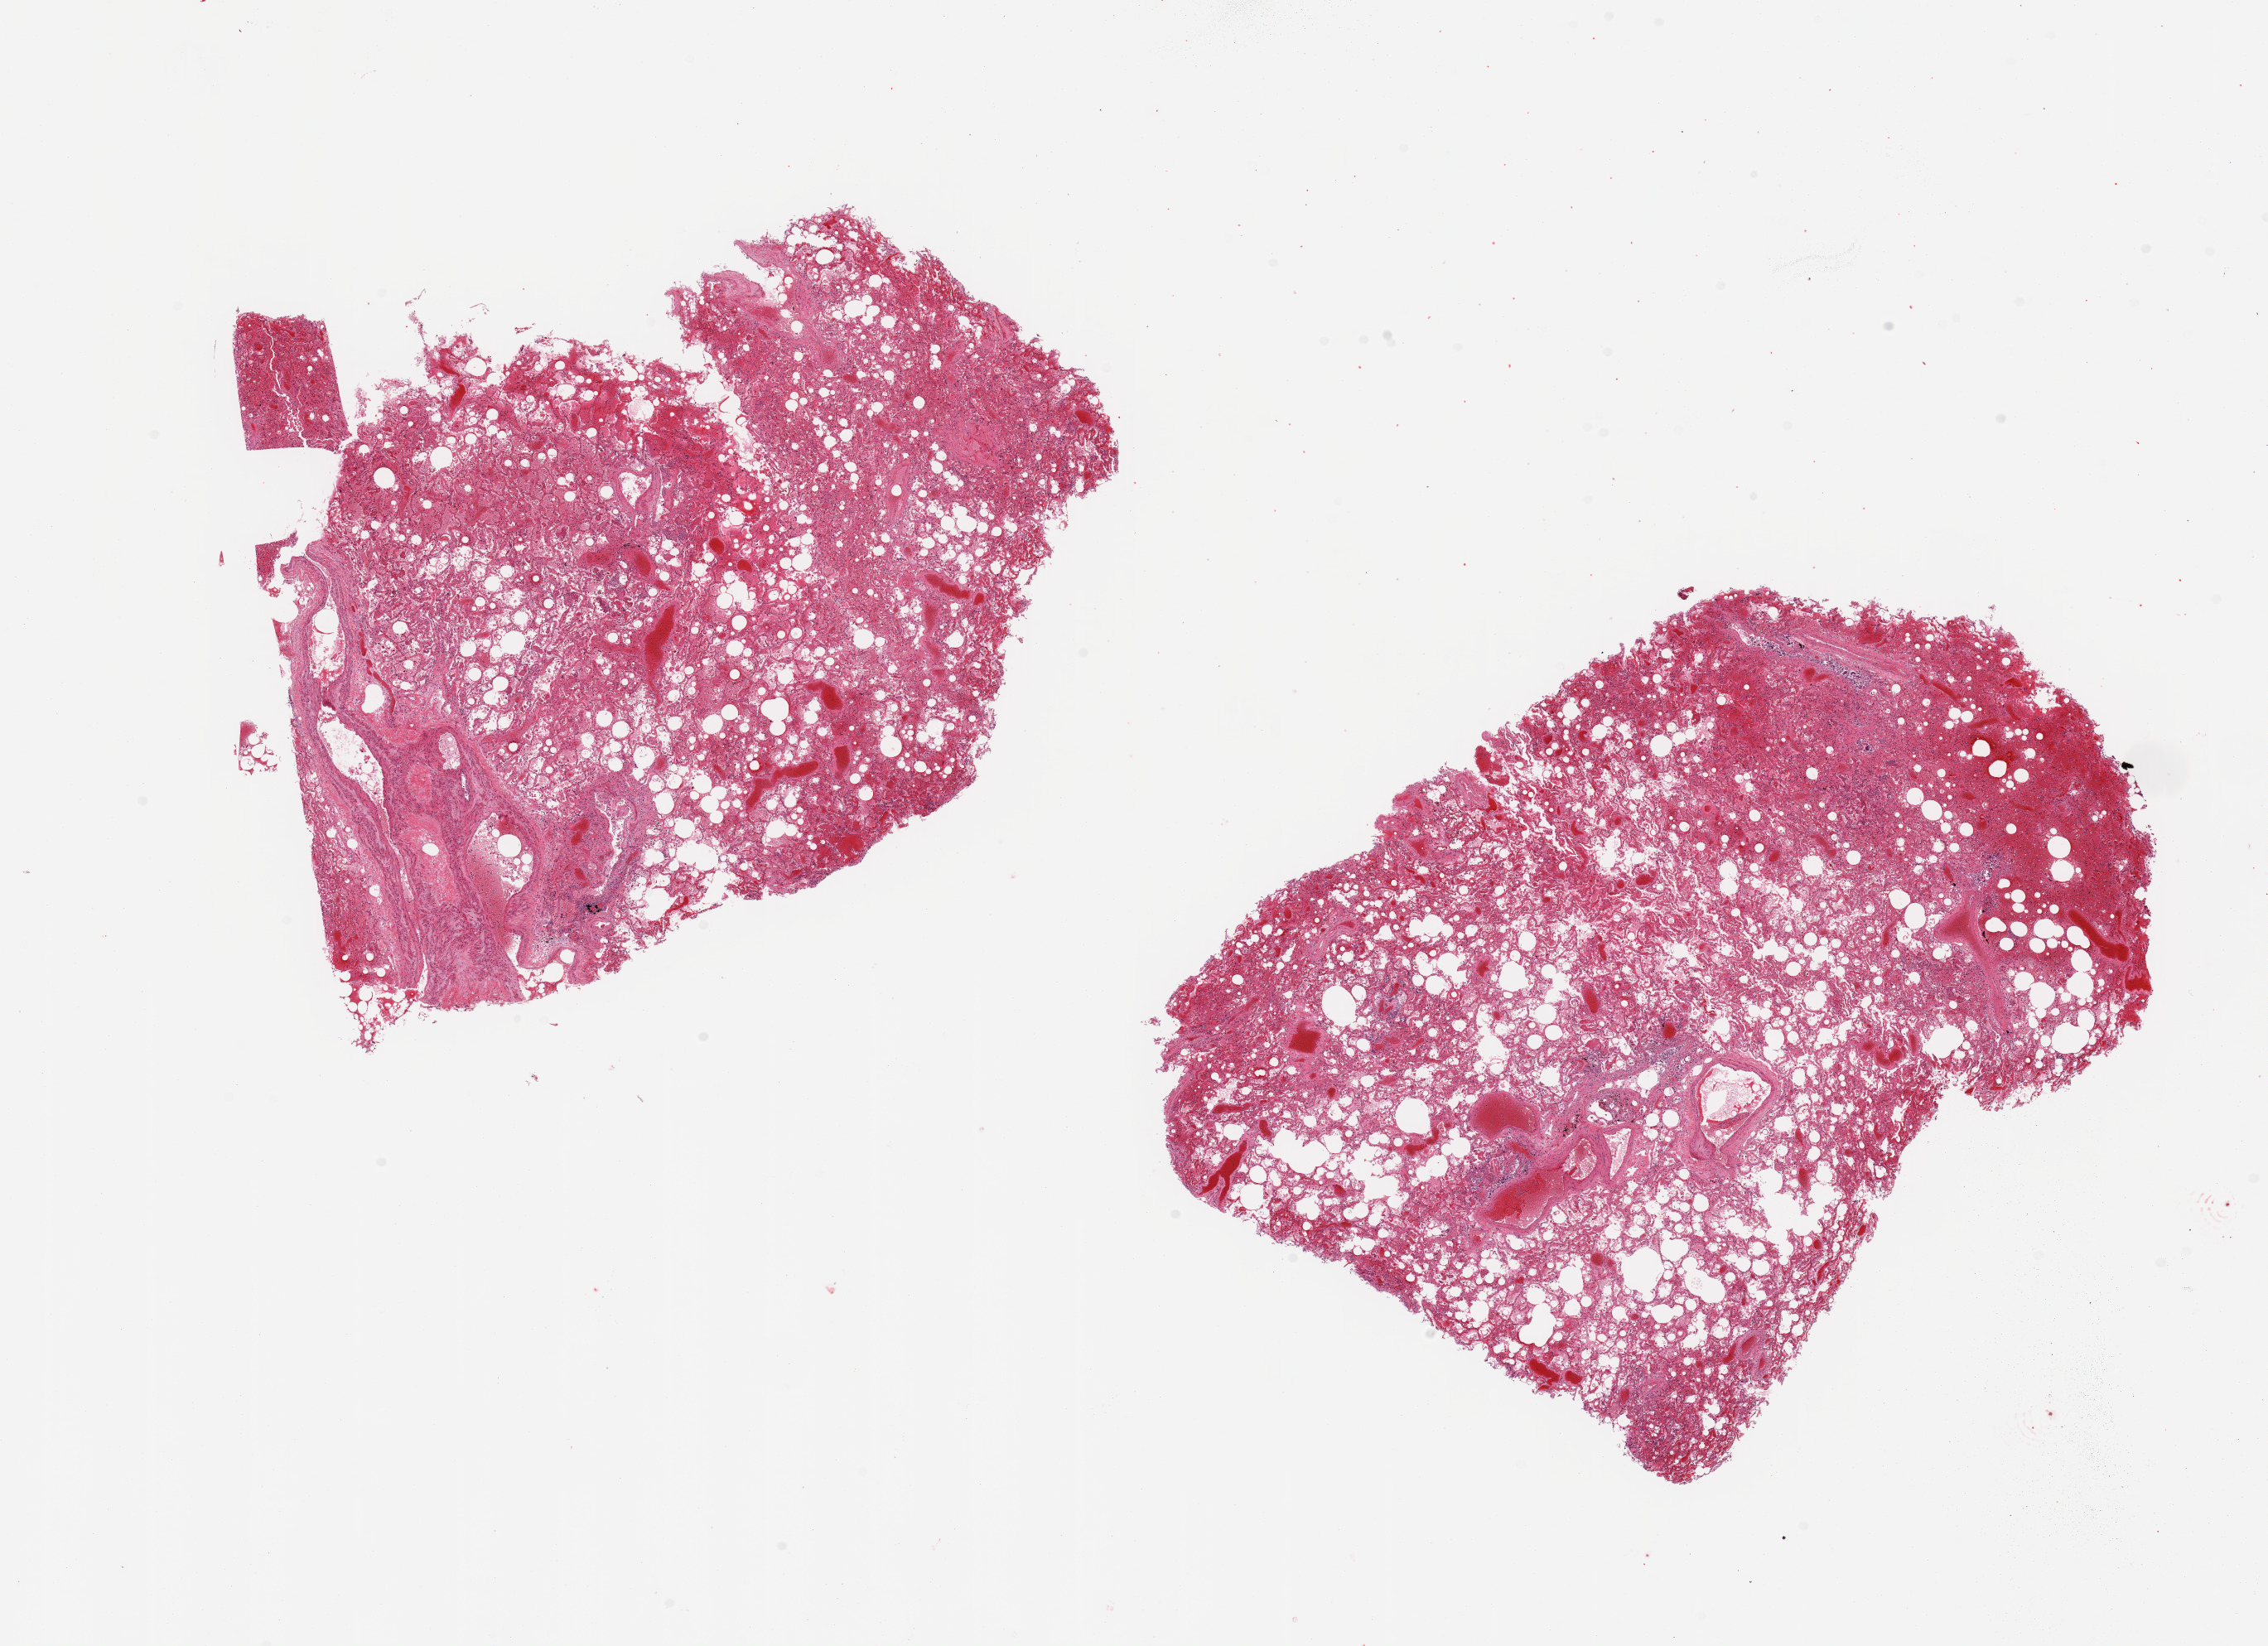
Haematoxylin and eosin whole-slide image, whole scanned area (about 21.7 x 15.7 mm) shown as a low-resolution overview, PAXgene-fixed paraffin-embedded (PFPE) section, sampled site (target tissue): lung, tissue donor sample. Female donor.
Reviewer comment on this tissue sample: 2 pieces, moderate congestion.